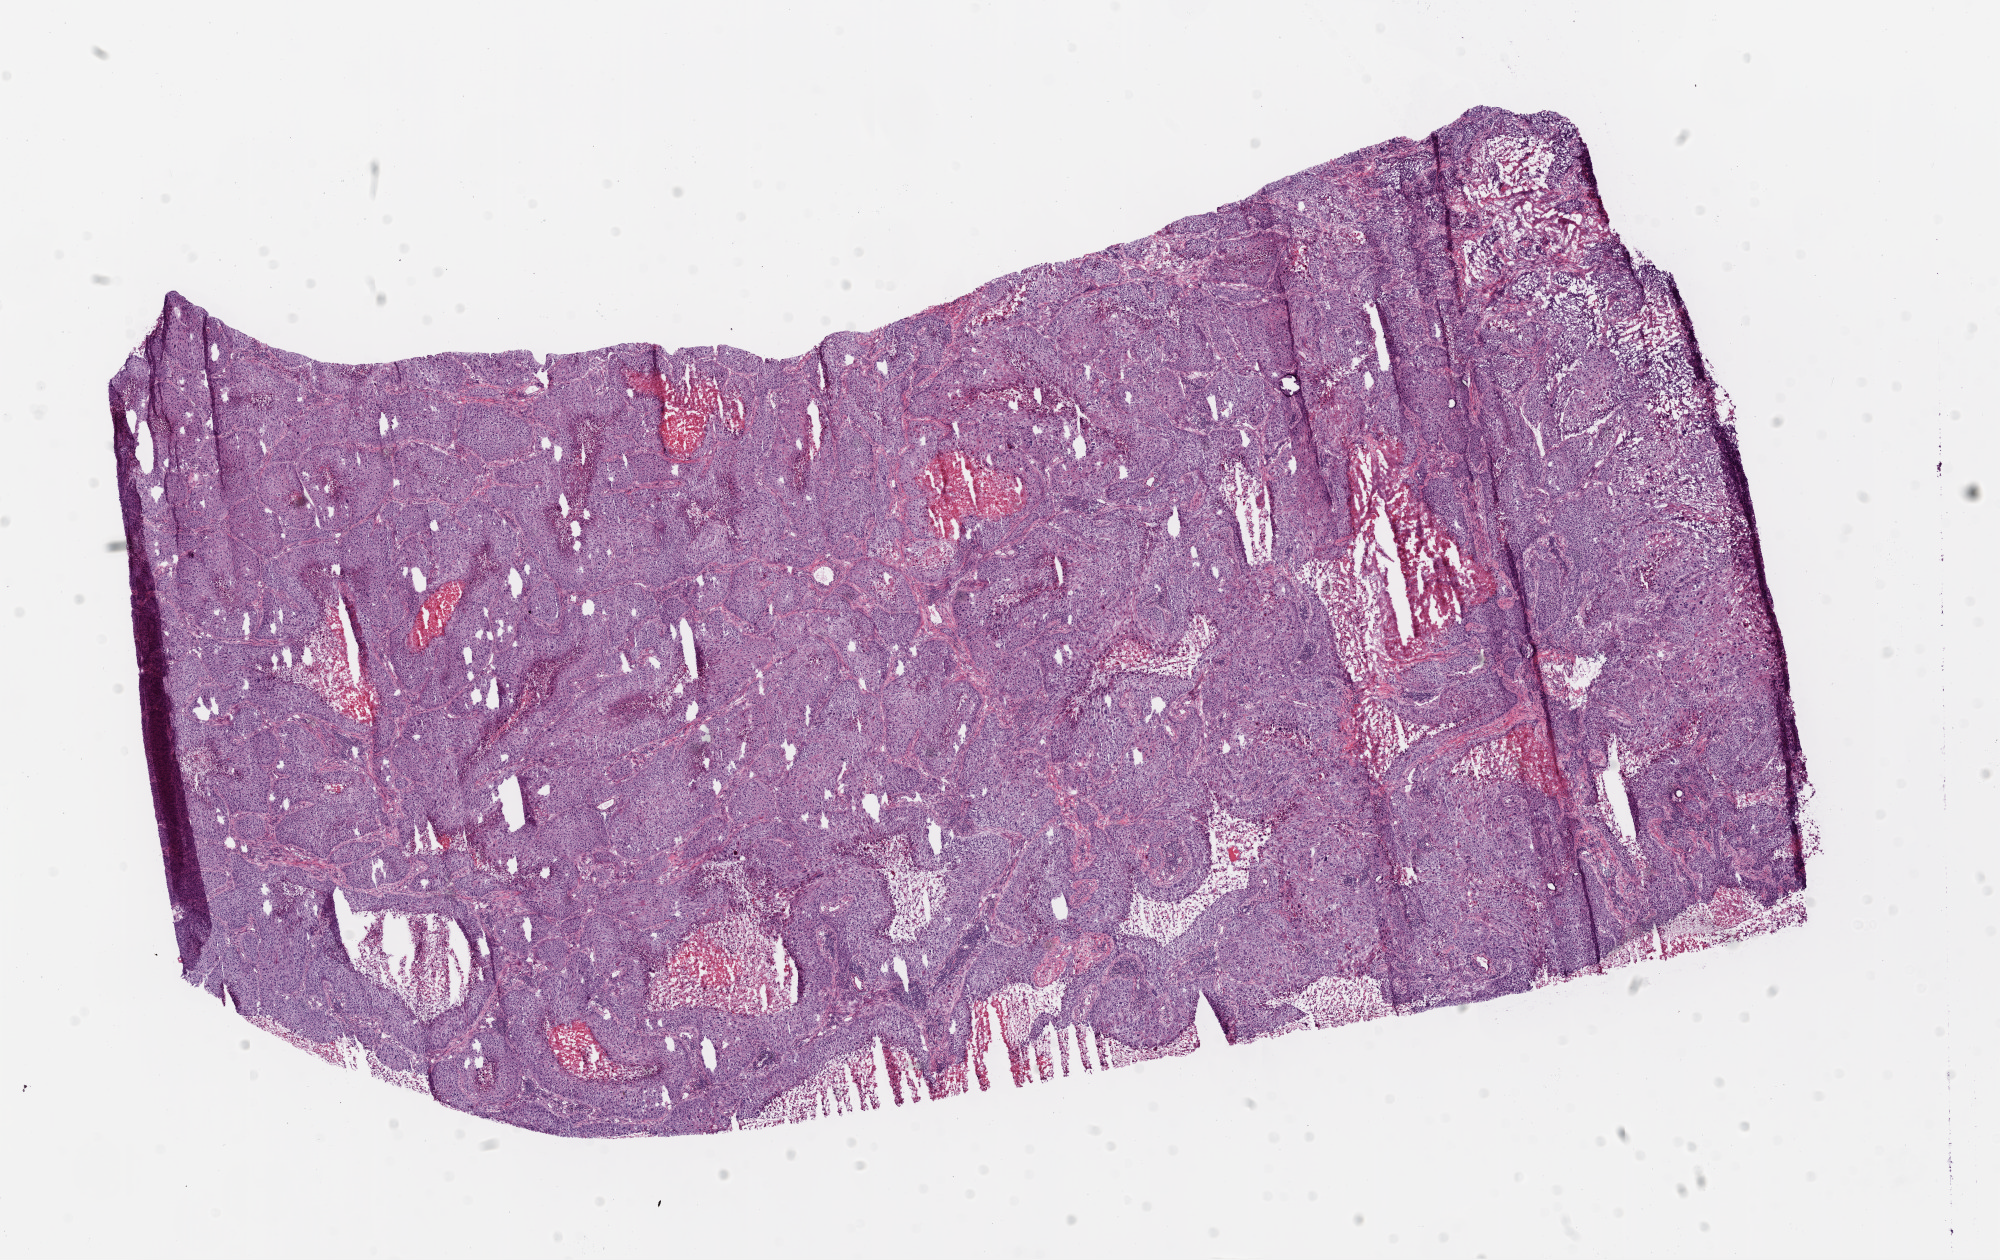
H&E whole-slide image — a low-resolution overview of the entire scanned area, about 16.0 x 10.1 mm, frozen section from the top of the tissue portion, primary tumour sample from the lung. Male, age 54 years at initial diagnosis. Pathologist review of this section (percent, as recorded): tumour cells 75%, tumour nuclei 90%, normal cells 0%, stromal cells 5%, necrosis 20%.
Diagnosis: Squamous cell carcinoma, NOS (upper lobe, lung). AJCC pathologic stage: IIIA. Laterality: left.